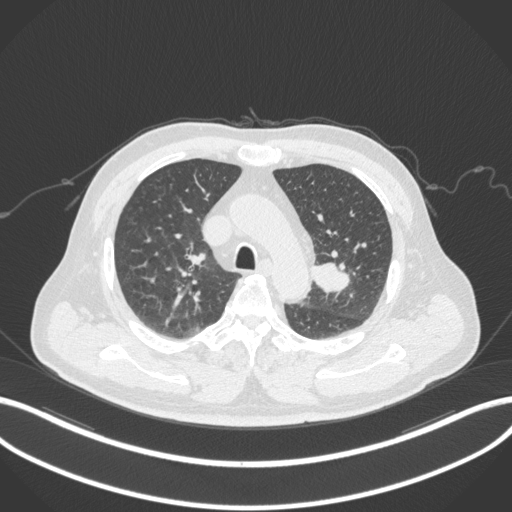
Chest CT, one axial slice; slice 215 of 286 in the series (ordered by position); reconstruction kernel B31f; 120 kVp; lung window (W 1500 / L -600 HU); 1 mm slice thickness; 512 × 512 image matrix. Patient: male, 67 years. From the clinical record (not read from this slice): clinical TNM (as recorded): T2a N1 M0; histopathological grade: G3.
Annotated regions visible in this slice (bounding box drawn by a radiologist):
- lung tumour (recorded histology: adenocarcinoma): bounding box [x1, y1, x2, y2] px = [309, 259, 352, 298]